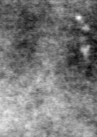
Crop from a digitized film mammogram around one marked abnormality, right breast, MLO view.
- Calcifications, morphology punctate, distribution clustered; BI-RADS assessment category 3; pathology (as recorded): malignant.